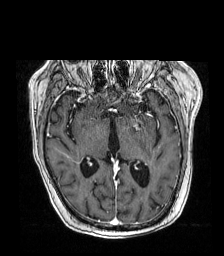
Brain MRI from a brain-tumour surgery series, one axial slice; T1-weighted post-contrast; 1 mm slice thickness; 224 × 256 image matrix, field of view 219 × 250 mm. Case-level facts recorded for this patient, not image findings: histopathology: Metastatic carcinoma from lung primary; tumour location: Left Frontal Caudate.
Structures marked on this image (manually delineated by an expert):
- tumour: bounding box <117,120,148,125> (left, top, right, bottom; pixels)